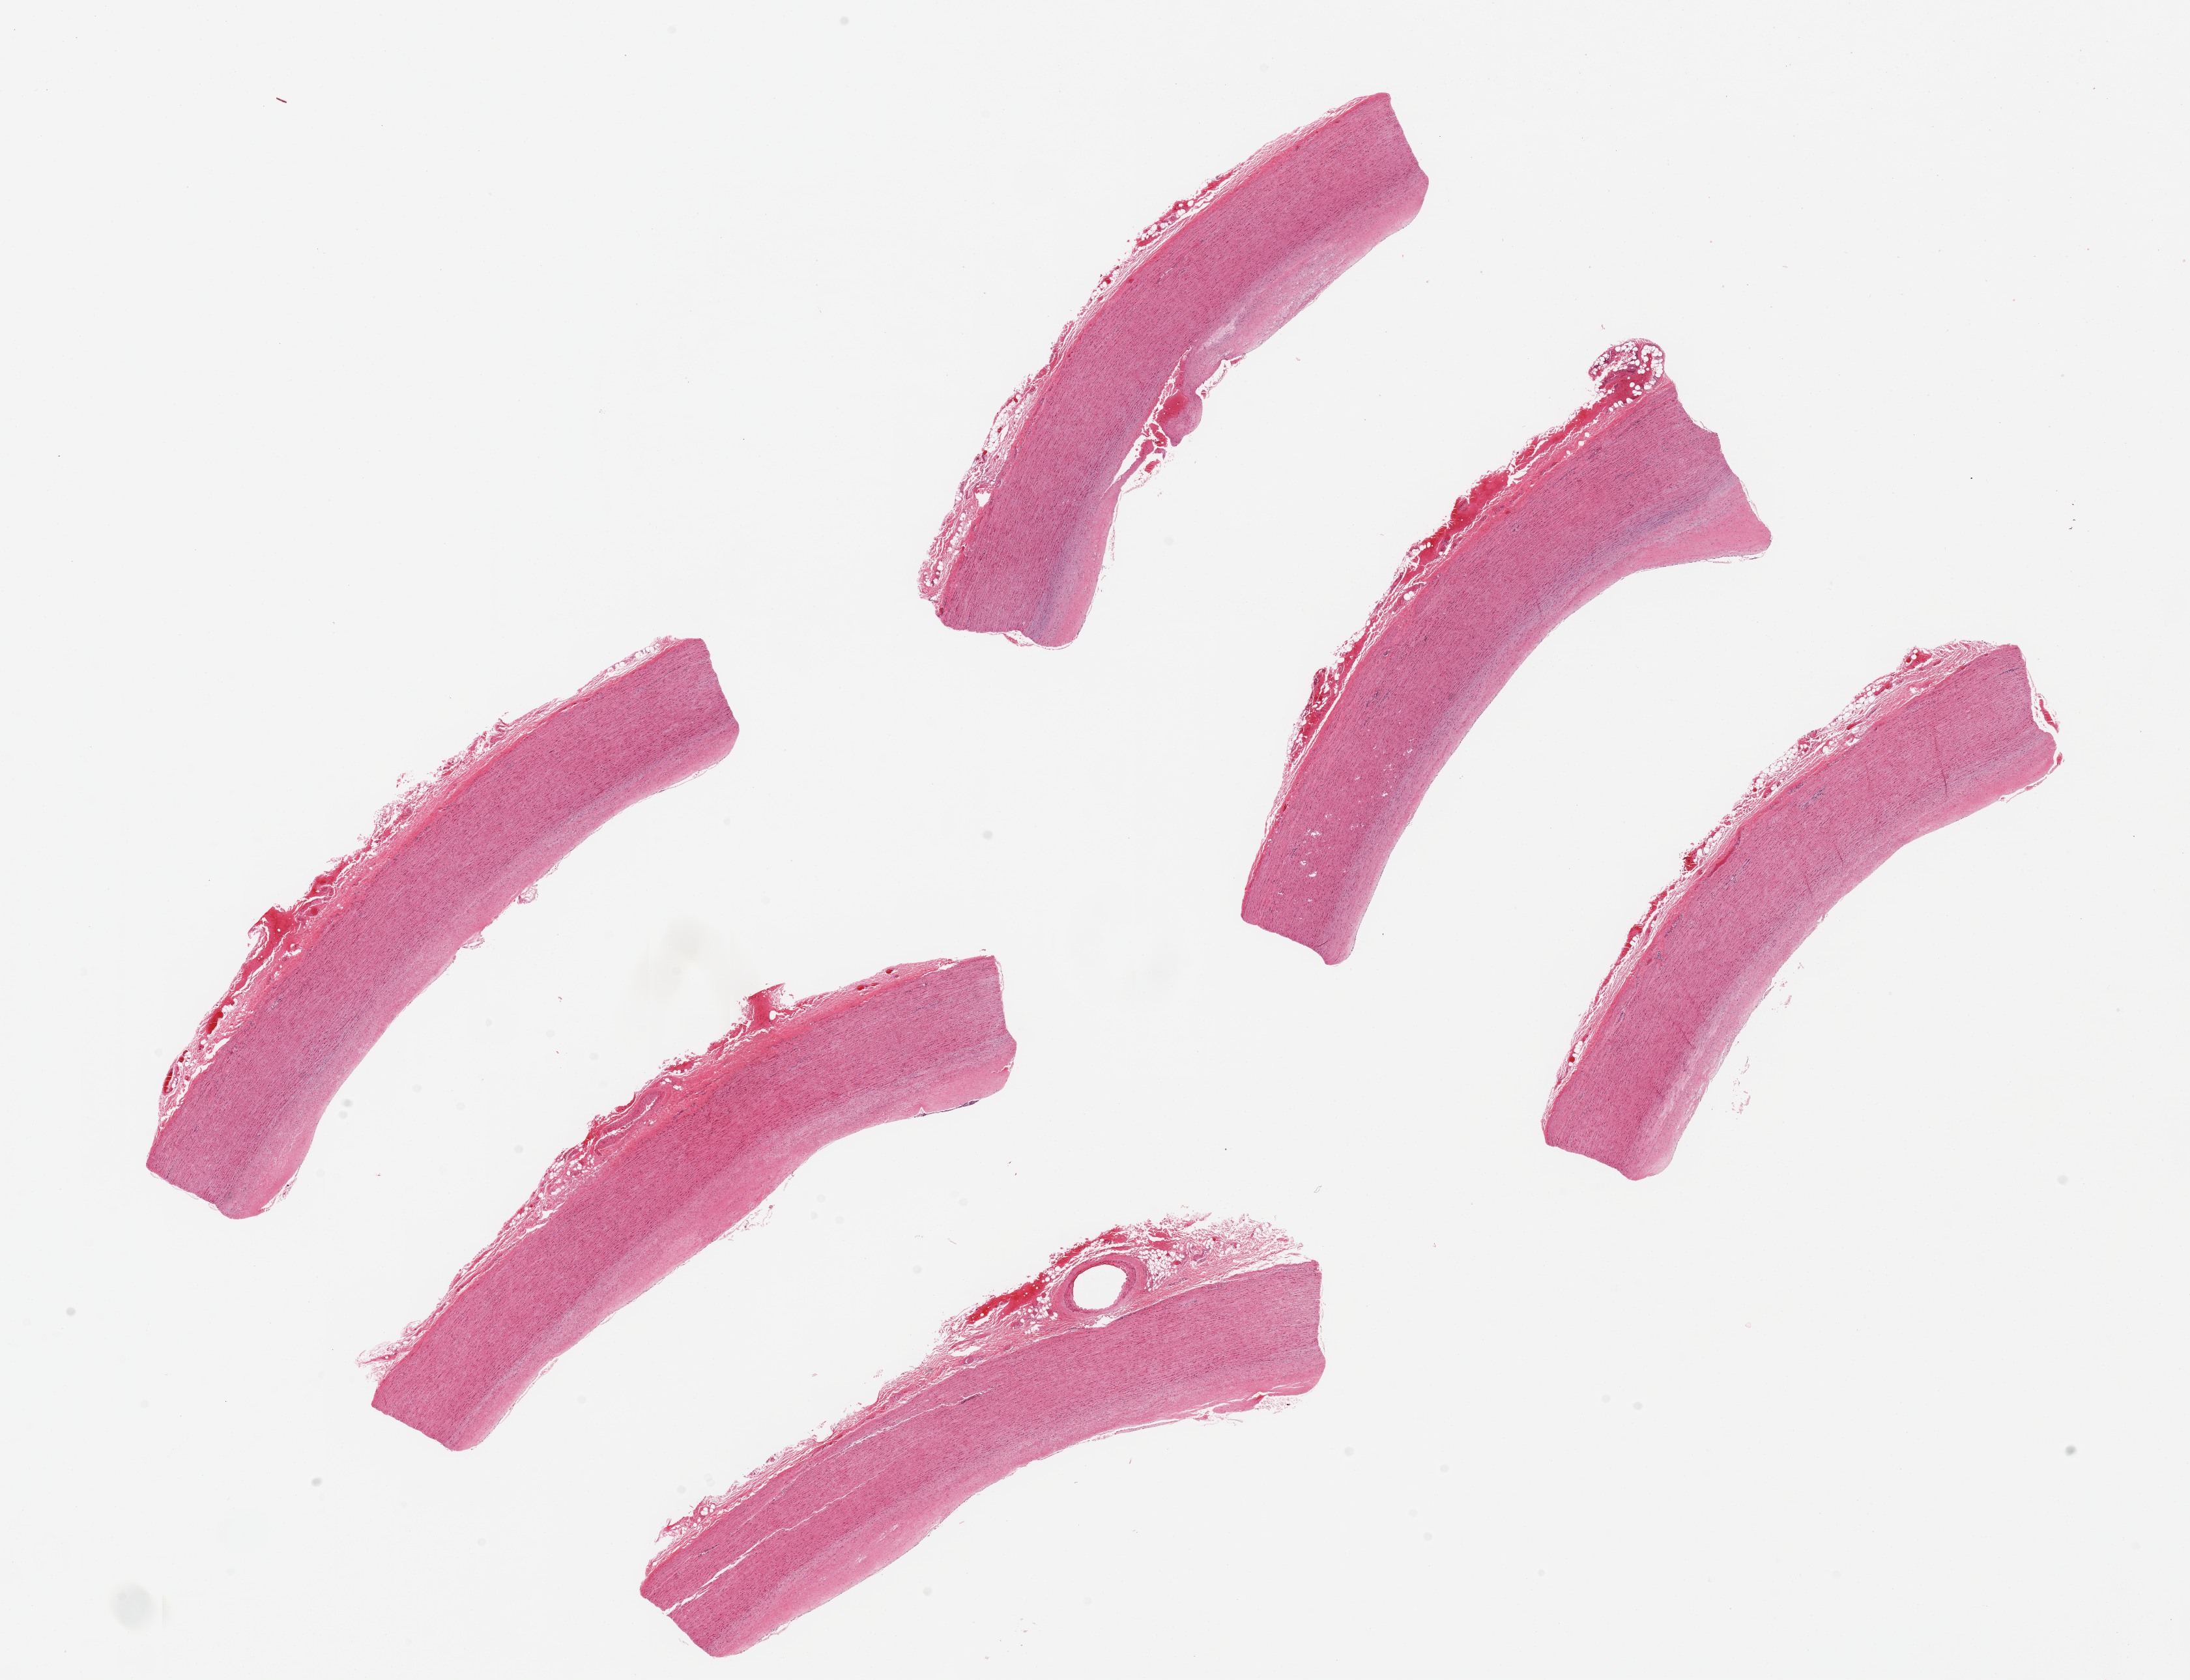
Digitized hematoxylin and eosin (H&E)-stained section, shown as a low-resolution overview of the whole scanned area (about 26.6 x 20.4 mm, from a 20x scan), PAXgene-fixed paraffin-embedded (PFPE) section, sampled site (target tissue): aorta, tissue donor sample. Donor: male.
Pathologist's review note for this sample: 6 pieces, ~9x1.5mm; focal plaques.